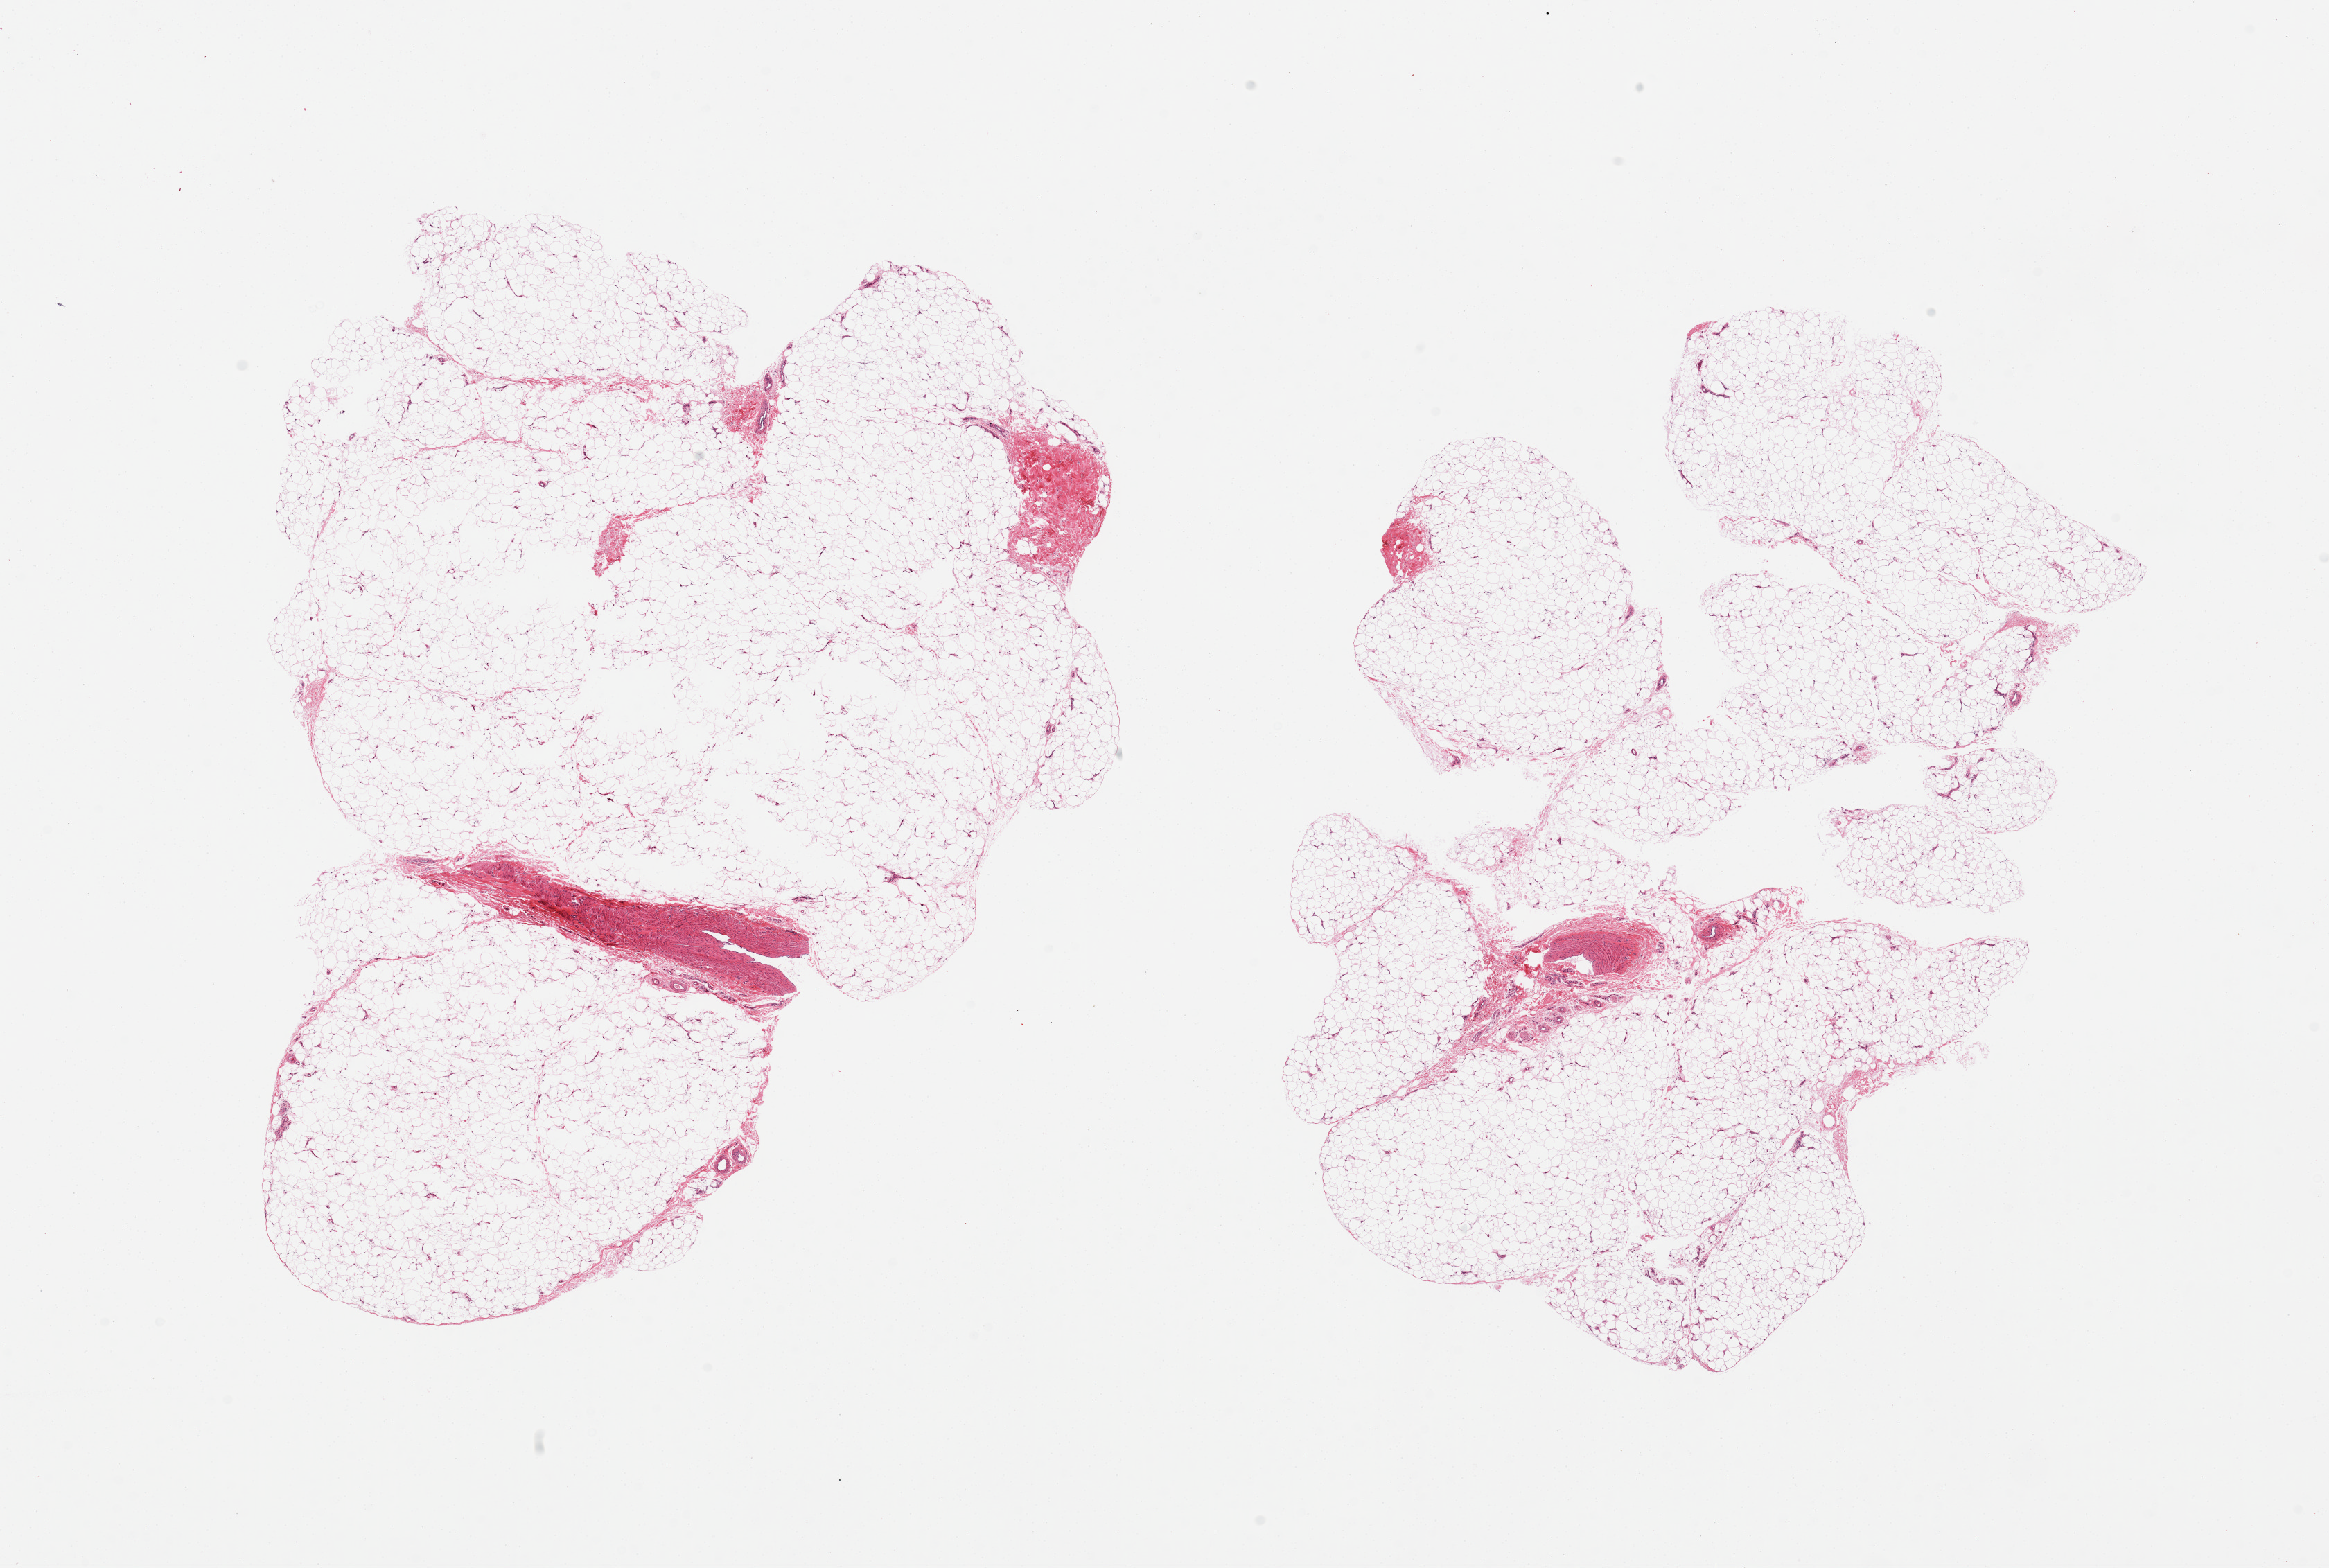
Digitized haematoxylin and eosin-stained section — low-resolution overview of the scanned area, about 26.6 x 17.9 mm. PAXgene-fixed paraffin-embedded (PFPE) section. Sampled site (target tissue): adipose tissue. Donor tissue sample.
Review note (as recorded): 2 pieces ~5% fibrous/fascial tissue.